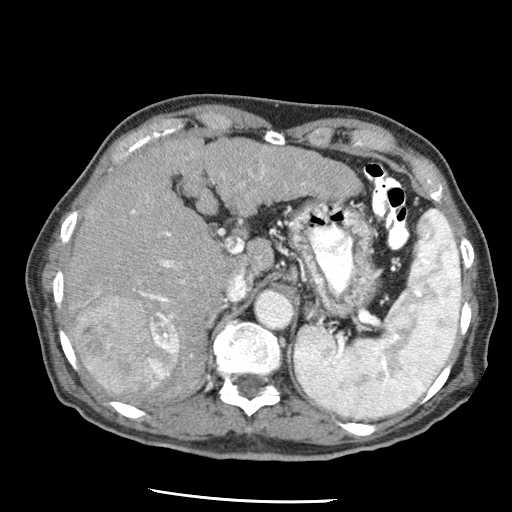
Contrast-enhanced abdominal CT (liver protocol), one axial slice. Position 37 of 79 along the scan axis. 120 kVp. Soft-tissue window (W 400 / L 40 HU). 2.5 mm slice thickness. 512 × 512 image matrix, field of view 320 × 320 mm. From the clinical record (not read from this slice): diagnosis: hepatocellular carcinoma (patient treated with transarterial chemoembolisation; whether this scan precedes or follows treatment is not stated here); TNM stage (as recorded): Stage-IIIA; Child-Pugh class: A; tumour nodularity: multinodular; tumour size: 7 cm.
Outlined on this slice (semi-automatic segmentation, software-assisted and operator-edited):
- liver parenchyma outside the tumour (the mass and vessels are separate outlines, so this box may not span the whole liver): bounding box <64,138,354,402> (left, top, right, bottom; pixels)
- mass: <74,296,180,396>
- liver vessels: <95,165,305,319>